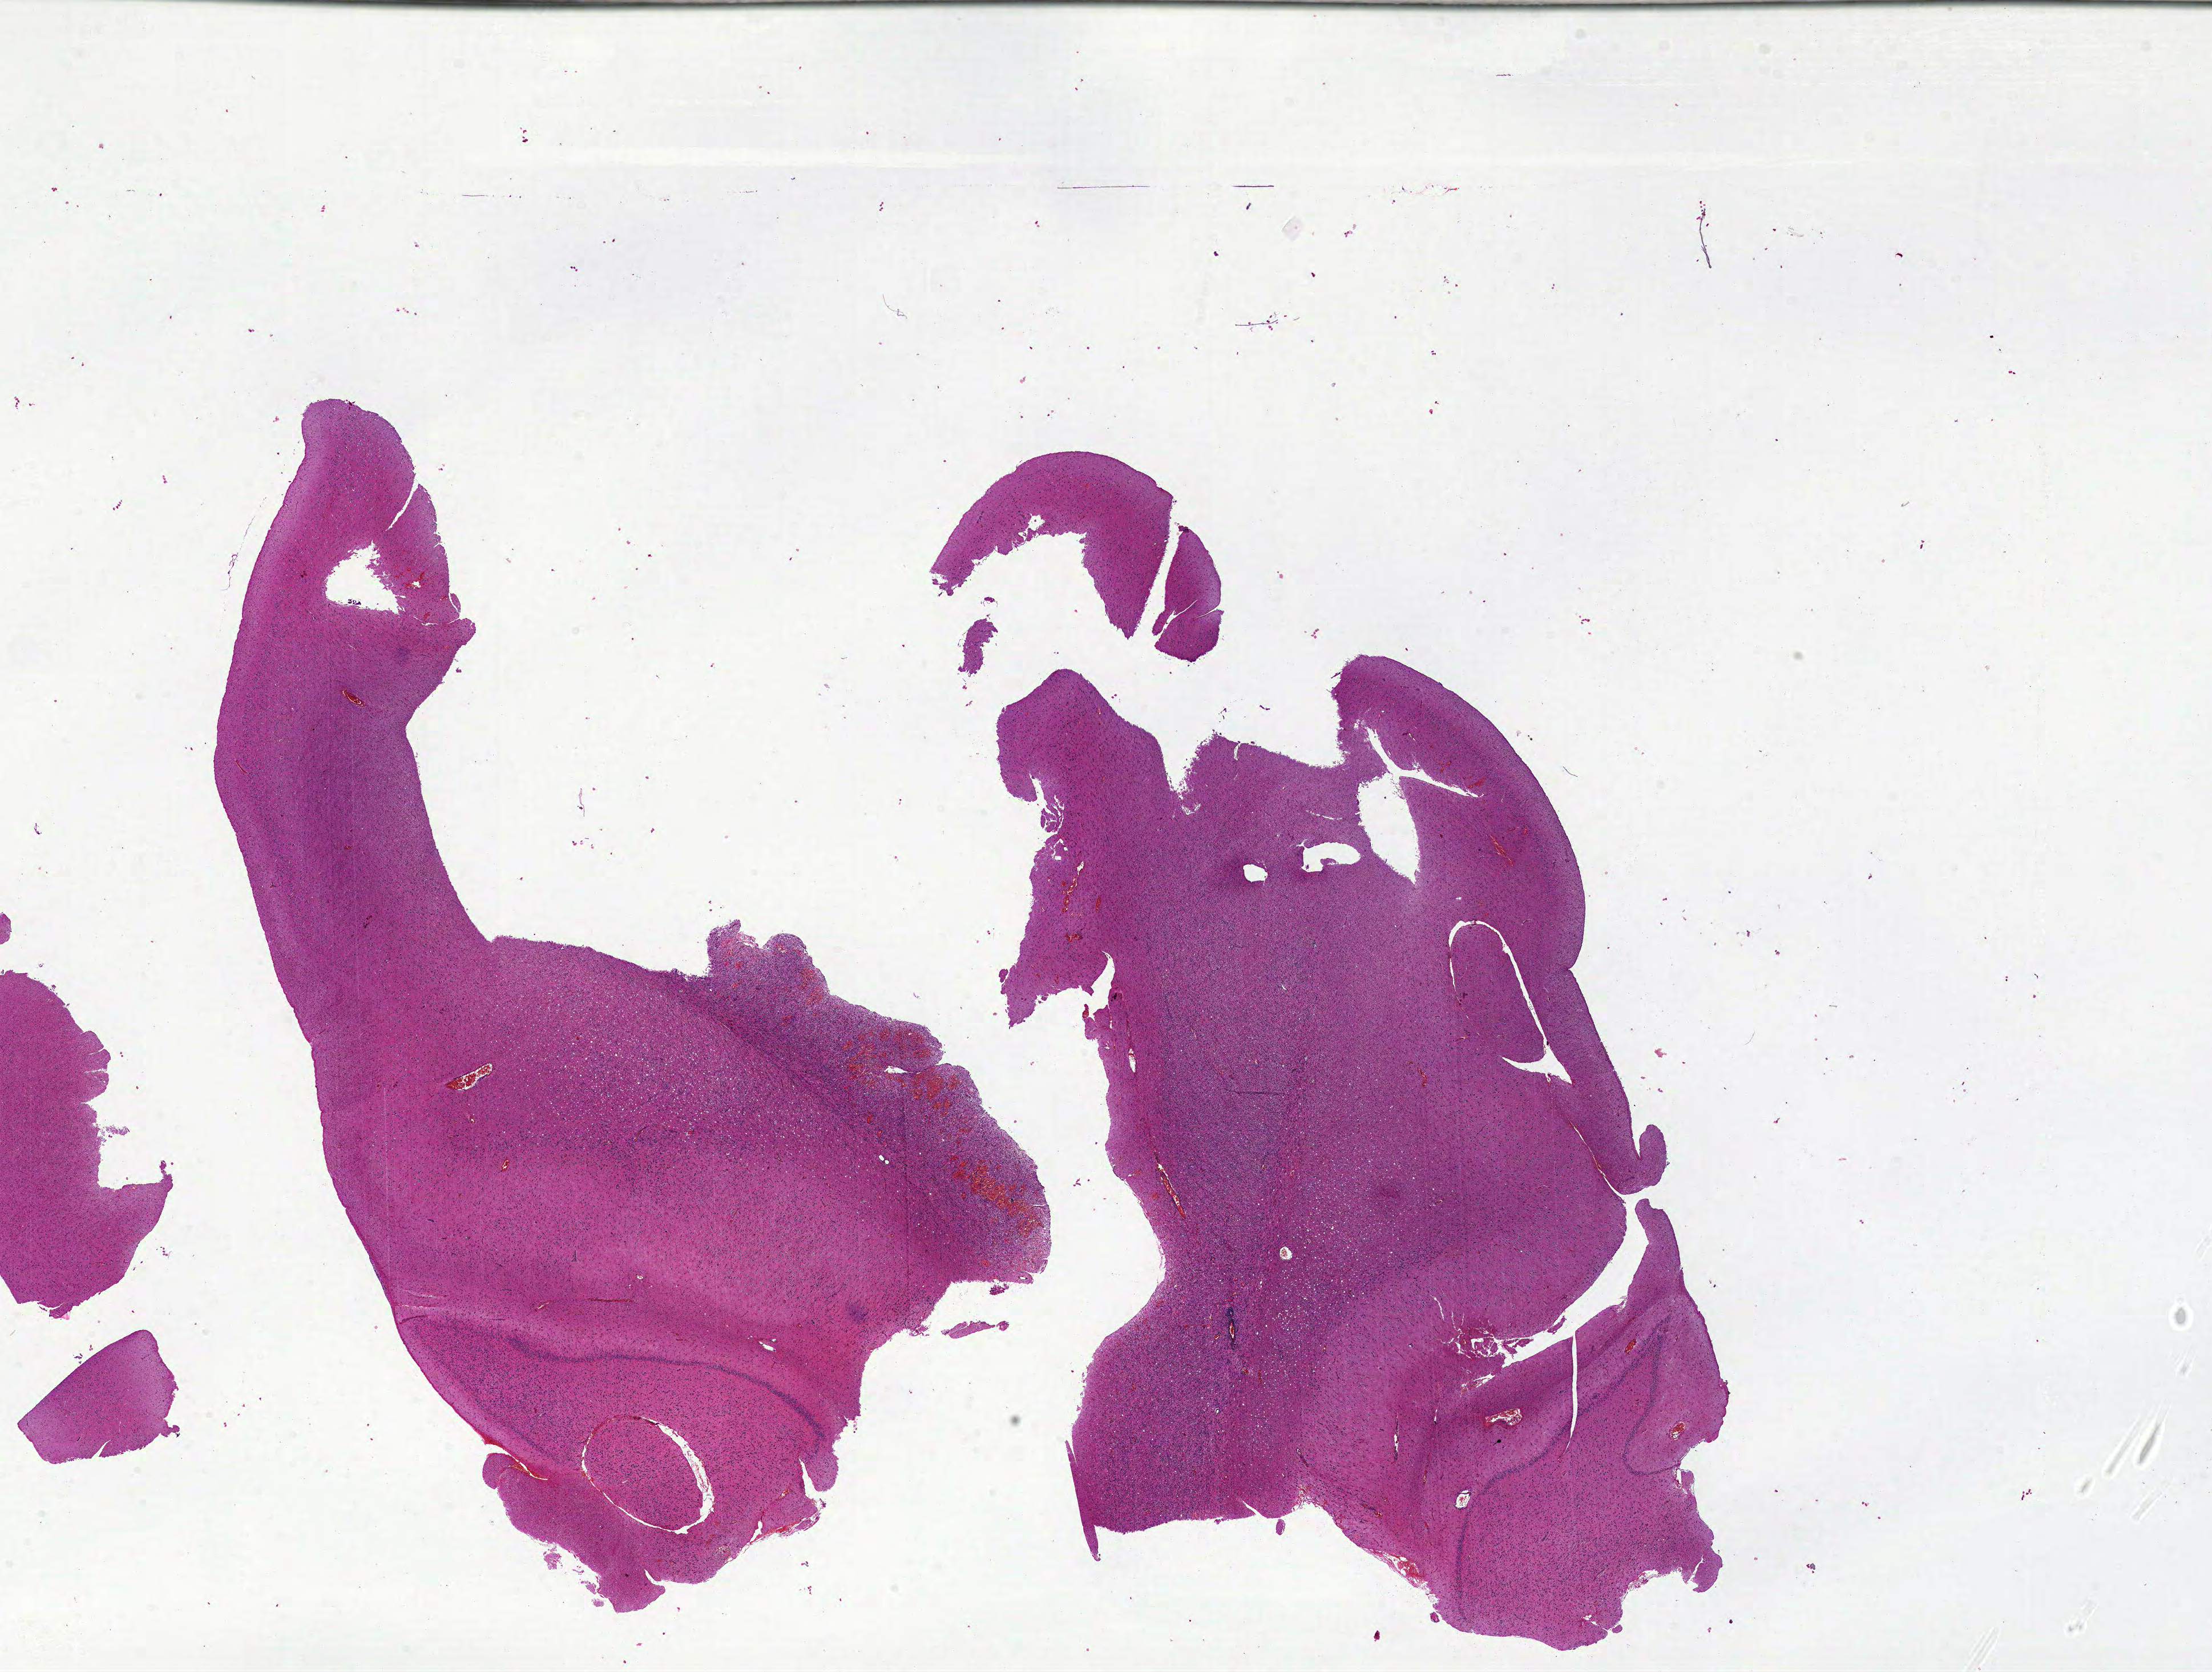
Digitized H&E tissue section (whole slide) — shown as a low-resolution overview of the whole scanned area (about 31.0 x 23.4 mm); FFPE section; primary tumour sample from the brain. Patient: male, age at initial diagnosis 46 years.
Histologic diagnosis: Glioblastoma.